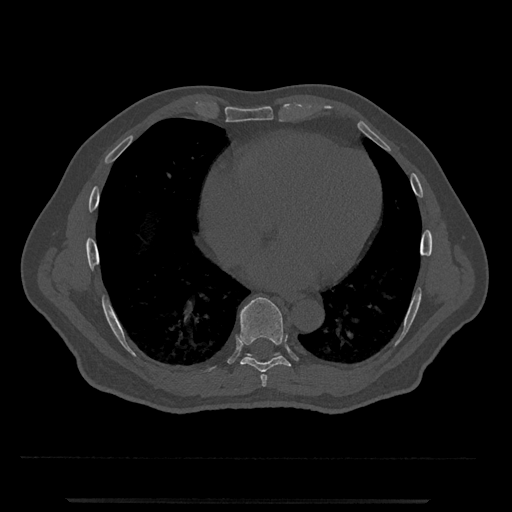
CT including the spine, one axial slice; position 621 of 797 along the scan axis; reconstruction kernel Br40s/3; 120 kVp; bone window (W 1800 / L 400 HU); 0.5 mm slice thickness; 512 × 512 image matrix, field of view 419 × 419 mm. Male patient, age 63 years. Case-level facts recorded for this patient, not image findings: primary cancer: prostate.
Annotated regions visible in this slice (semi-automatically segmented with operator editing):
- T7 vertebra: bounding box (x1, y1, x2, y2) in pixels: (260, 374, 267, 387)
- T8 vertebra: (239, 297, 291, 372)
- T9 vertebra: (246, 353, 280, 358)